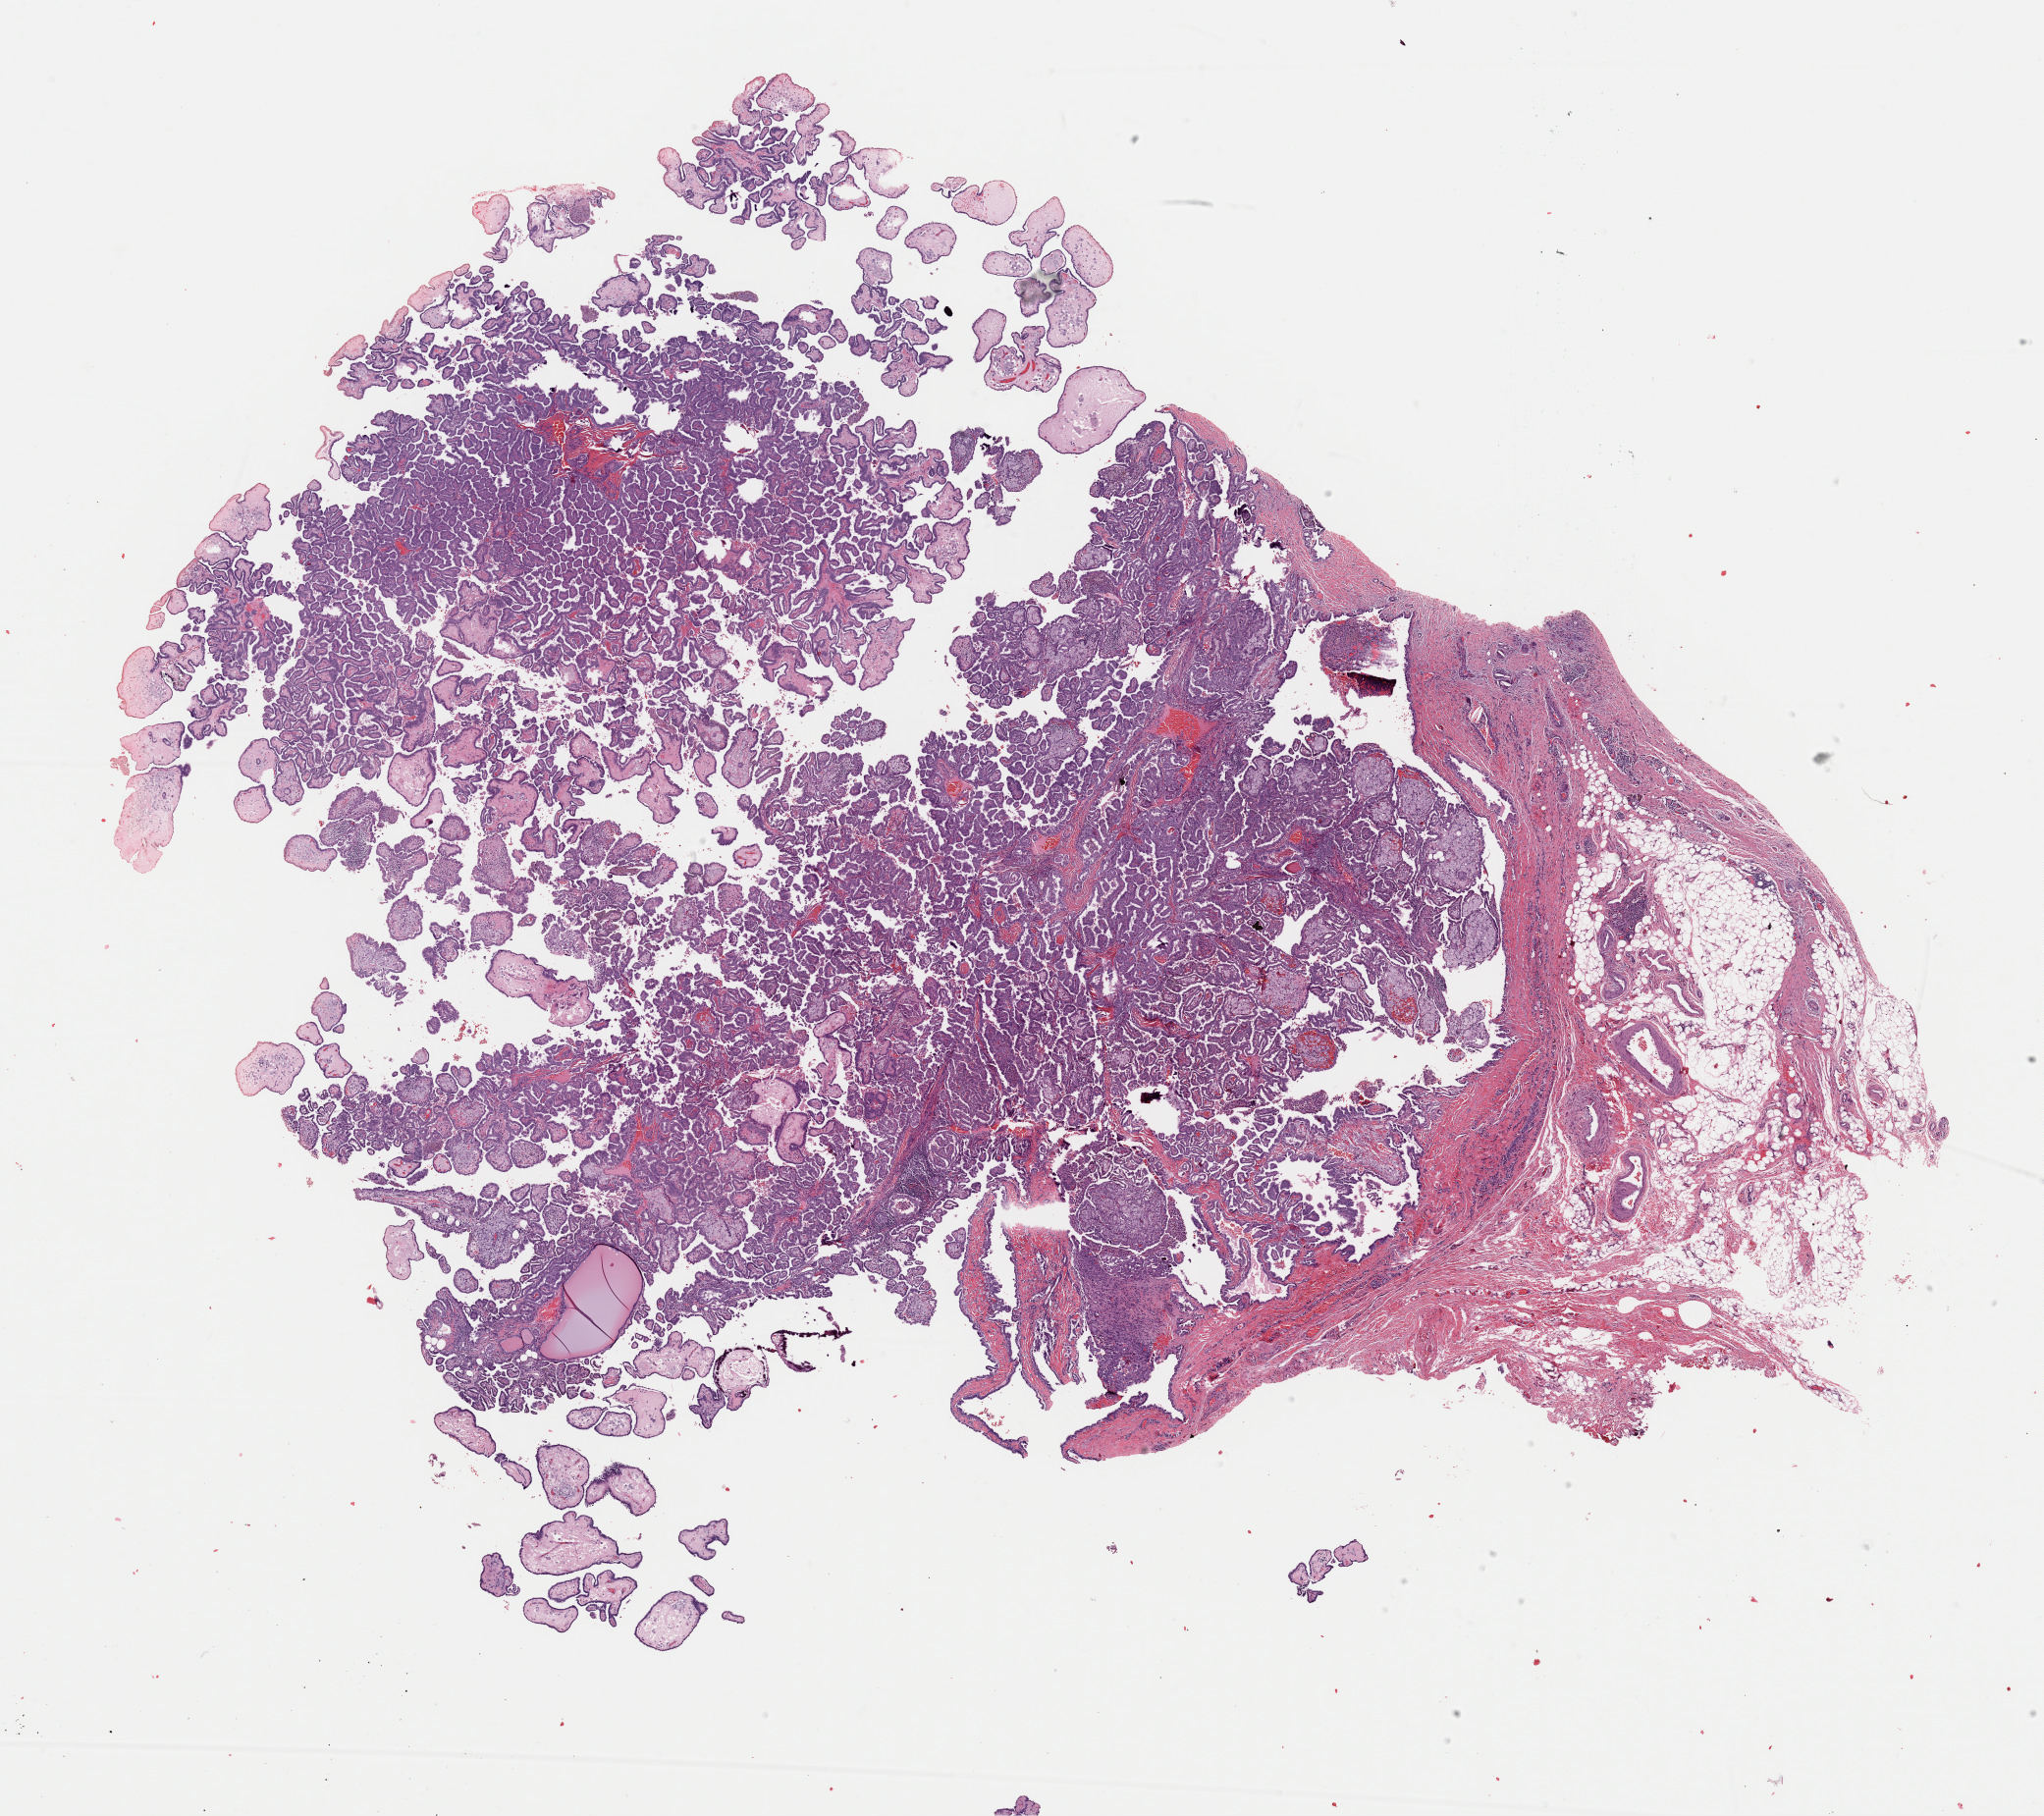
H&E-stained whole-slide image — shown as a low-resolution overview of the whole scanned area (about 16.4 x 14.6 mm); FFPE section; primary tumour sample from the thyroid. Patient: female, age at initial diagnosis 47 years.
Histologic diagnosis: Papillary adenocarcinoma, NOS (thyroid gland). AJCC pathologic stage: II.